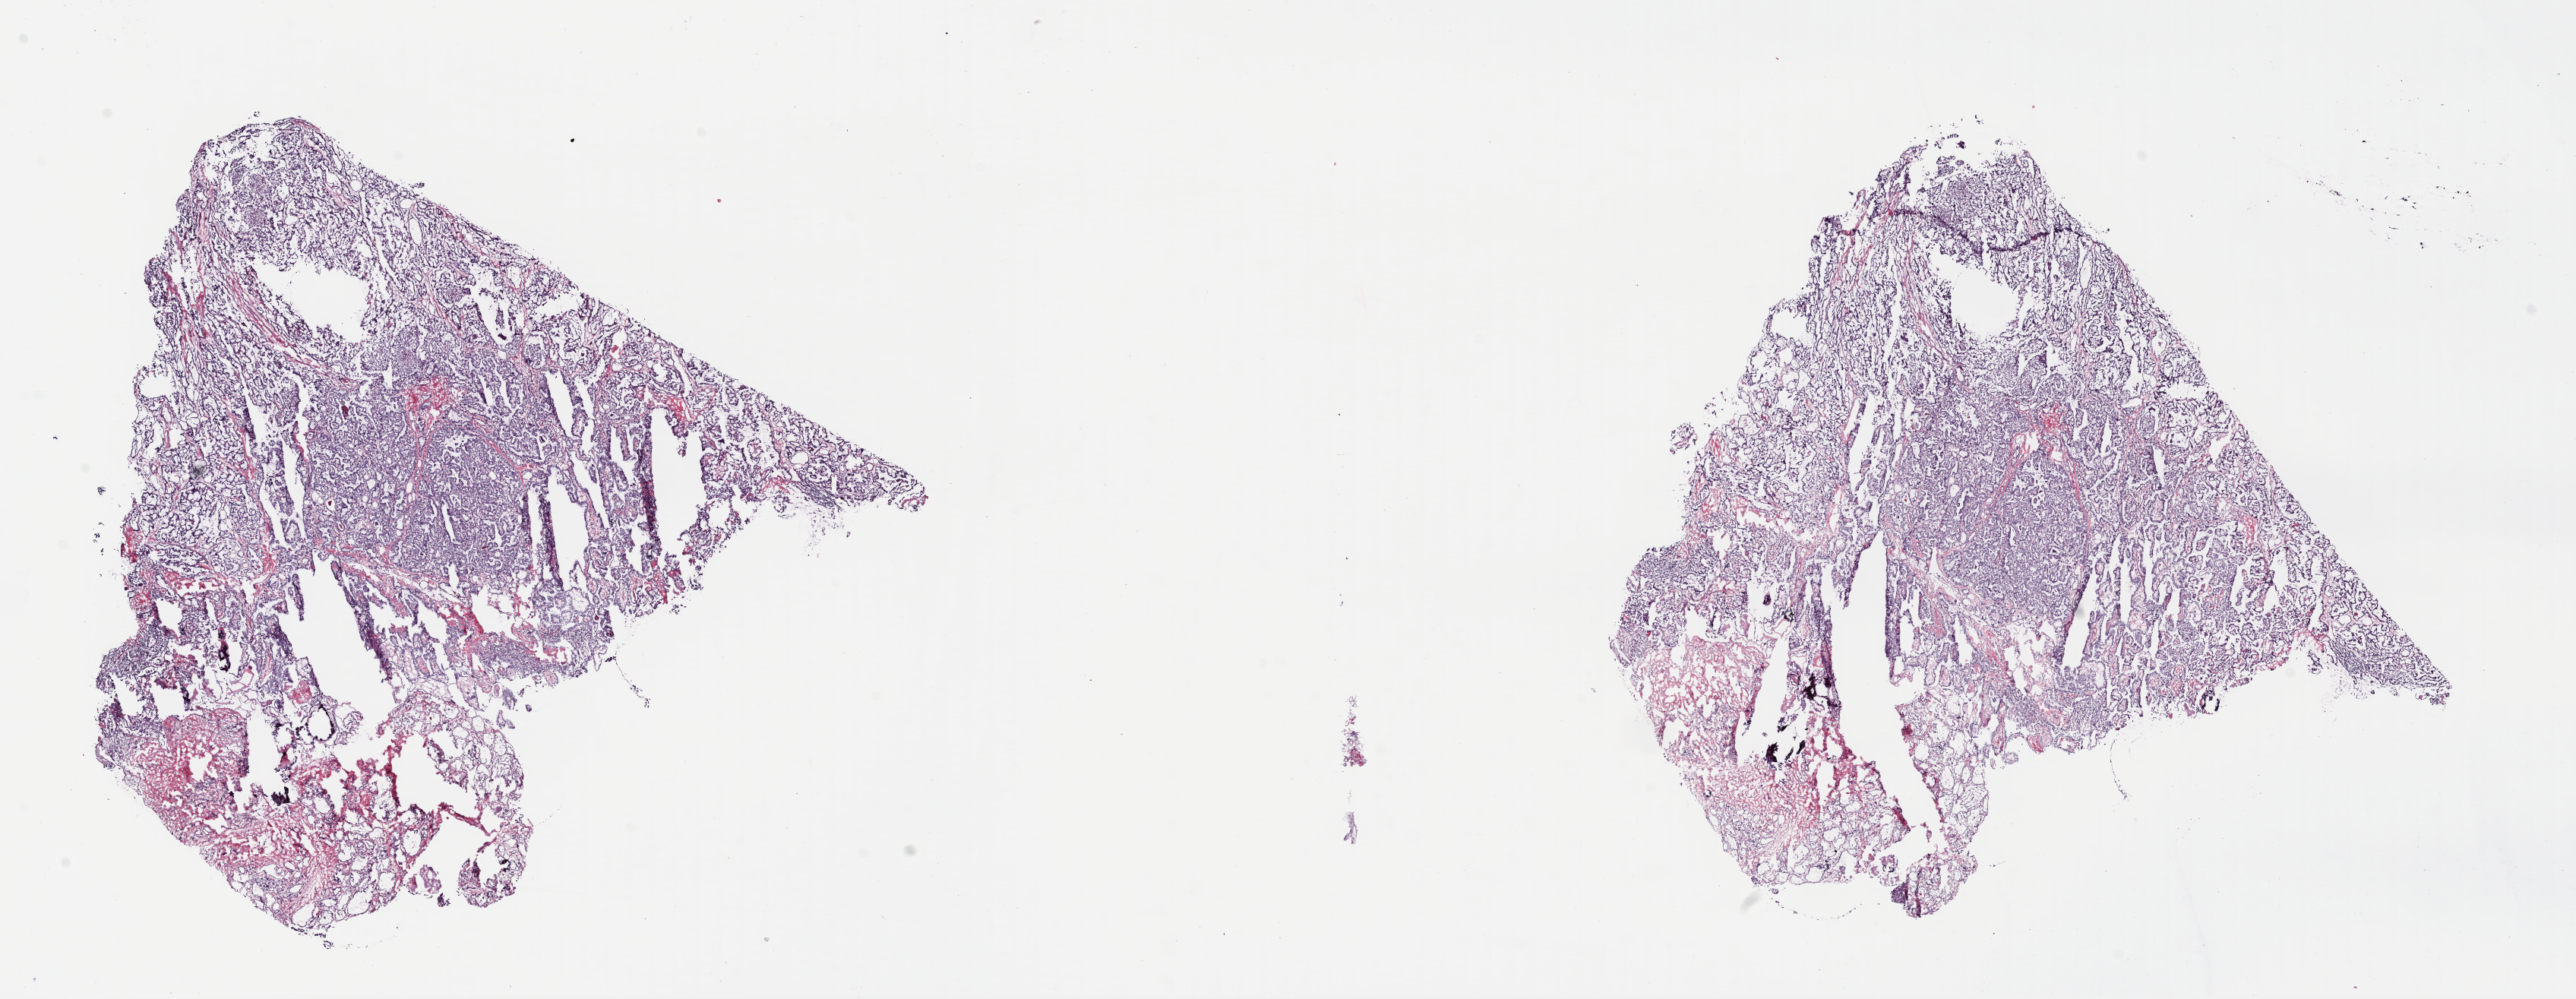
Digitized H&E-stained tissue section (whole slide) — low-resolution overview of the scanned area, about 26.7 x 10.3 mm, frozen section from the top of the tissue portion, sample: primary tumour, thyroid. Male, age 55 years at initial diagnosis. Slide review estimates, as recorded: tumour cells 70%, tumour nuclei 70%, normal cells 5%, stromal cells 25%, necrosis 0%. Infiltration values recorded for this section: lymphocyte infiltration 5%, monocyte infiltration 0%, neutrophil infiltration 0%.
Pathologic diagnosis: Papillary adenocarcinoma, NOS (thyroid gland). Laterality: right. Lymph nodes positive (case pathology): 30 of 82 examined. AJCC pathologic stage: IVA (7th edition).